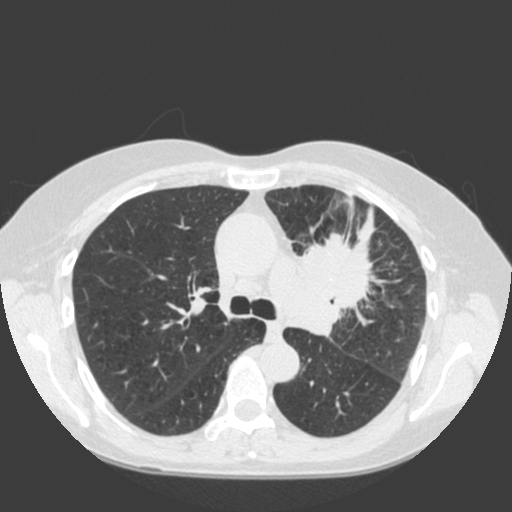
Axial slice from a low-dose chest CT screening exam, first (baseline) screen, lung window (W 1500 / L -600 HU), standard (soft-tissue) reconstruction kernel (C), slice 60 of 184 in the series. Female, age 66 years at enrolment.
- Lesion marked by an expert reader, bounding box [x1, y1, x2, y2] px = [281, 222, 399, 328].
- Screening reader's record for this exam (one nodule recorded; not confirmed to be the boxed lesion): non-calcified nodule or mass ≥4 mm, left upper lobe, 61 × 45 mm, spiculated (stellate) margins, soft tissue attenuation.
- Official screen result: positive, change unspecified: nodule(s) >= 4 mm or enlarging nodule(s), mass(es), or other non-specific abnormalities suspicious for lung cancer.
- Participant outcome: lung cancer diagnosed 19 days after this screen — squamous cell carcinoma, keratinizing, NOS, left upper lobe, left hilum, mediastinum, left main stem bronchus, other location, poorly differentiated (G3), stage IIIB (AJCC 6th edition), 60 mm at pathology.